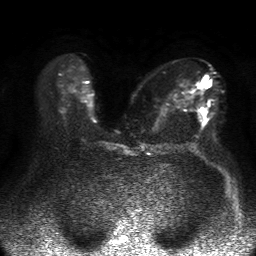
Breast MRI, one axial slice; slice 24 of 50 in the series (ordered by position); diffusion-weighted series; image 2 of 4 stored at this slice position (different b-values; order by instance number); 1.5 T; 4 mm slice thickness; 256 × 256 image matrix, field of view 360 × 360 mm. Female patient.
Annotated regions visible in this slice (expert manual segmentation):
- tumour on diffusion-weighted imaging: bounding box [x1, y1, x2, y2] px = [201, 76, 210, 115]